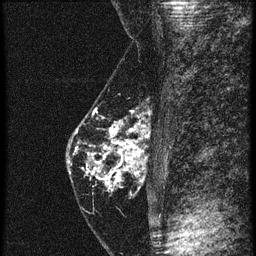
Breast MRI (dynamic contrast-enhanced), one sagittal slice; position 22 of 60 along the scan axis; 4 images stored at this slice position (order not interpretable as contrast timing); 1.5 T; TE 4.2 ms, TR 20.4 ms; 1.5 mm slice thickness; 256 × 256 image matrix, field of view 180 × 180 mm. Female patient, age 46 years. Case-level facts recorded for this patient, not image findings: setting: breast cancer imaged before/during neoadjuvant chemotherapy; receptor status: triple-negative.
Annotated regions visible in this slice (semi-automatic segmentation, software-assisted and operator-edited):
- analysis volume of interest (the breast-tissue region the enhancement analysis was run in; not a lesion): bounding box [x1, y1, x2, y2] px = [67, 82, 145, 201]
- tumour enhancement mask (voxels above the 90 % enhancement threshold inside the analysis volume of interest): [77, 122, 144, 187]